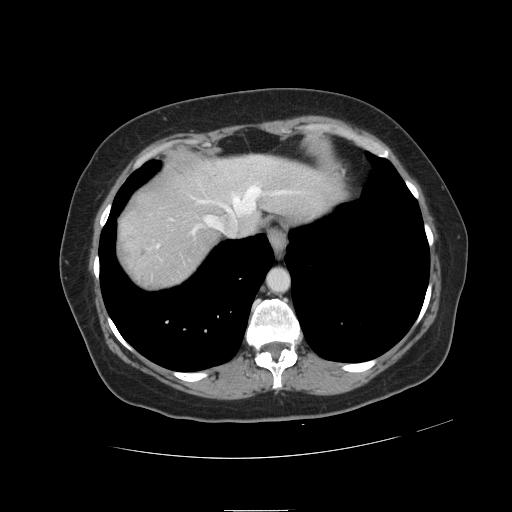
Contrast-enhanced abdominal CT, one axial slice. Position 104 of 121 along the scan axis. Intravenous contrast given. Soft-tissue window (W 400 / L 40 HU). 512 × 512 image matrix, field of view 400 × 400 mm. Female patient, age 52 years. From the clinical record (not read from this slice): diagnosis: colorectal cancer liver metastases, imaged before liver resection; multiple liver metastases: yes; largest metastasis: 6.3 cm; chemotherapy before resection: yes.
Outlined on this slice (manually delineated by an expert):
- hepatic veins: bounding box (x1, y1, x2, y2) in pixels: (155, 186, 302, 249)
- liver: (117, 155, 337, 289)
- planned liver remnant (the part of the liver to remain after resection): (183, 155, 336, 227)